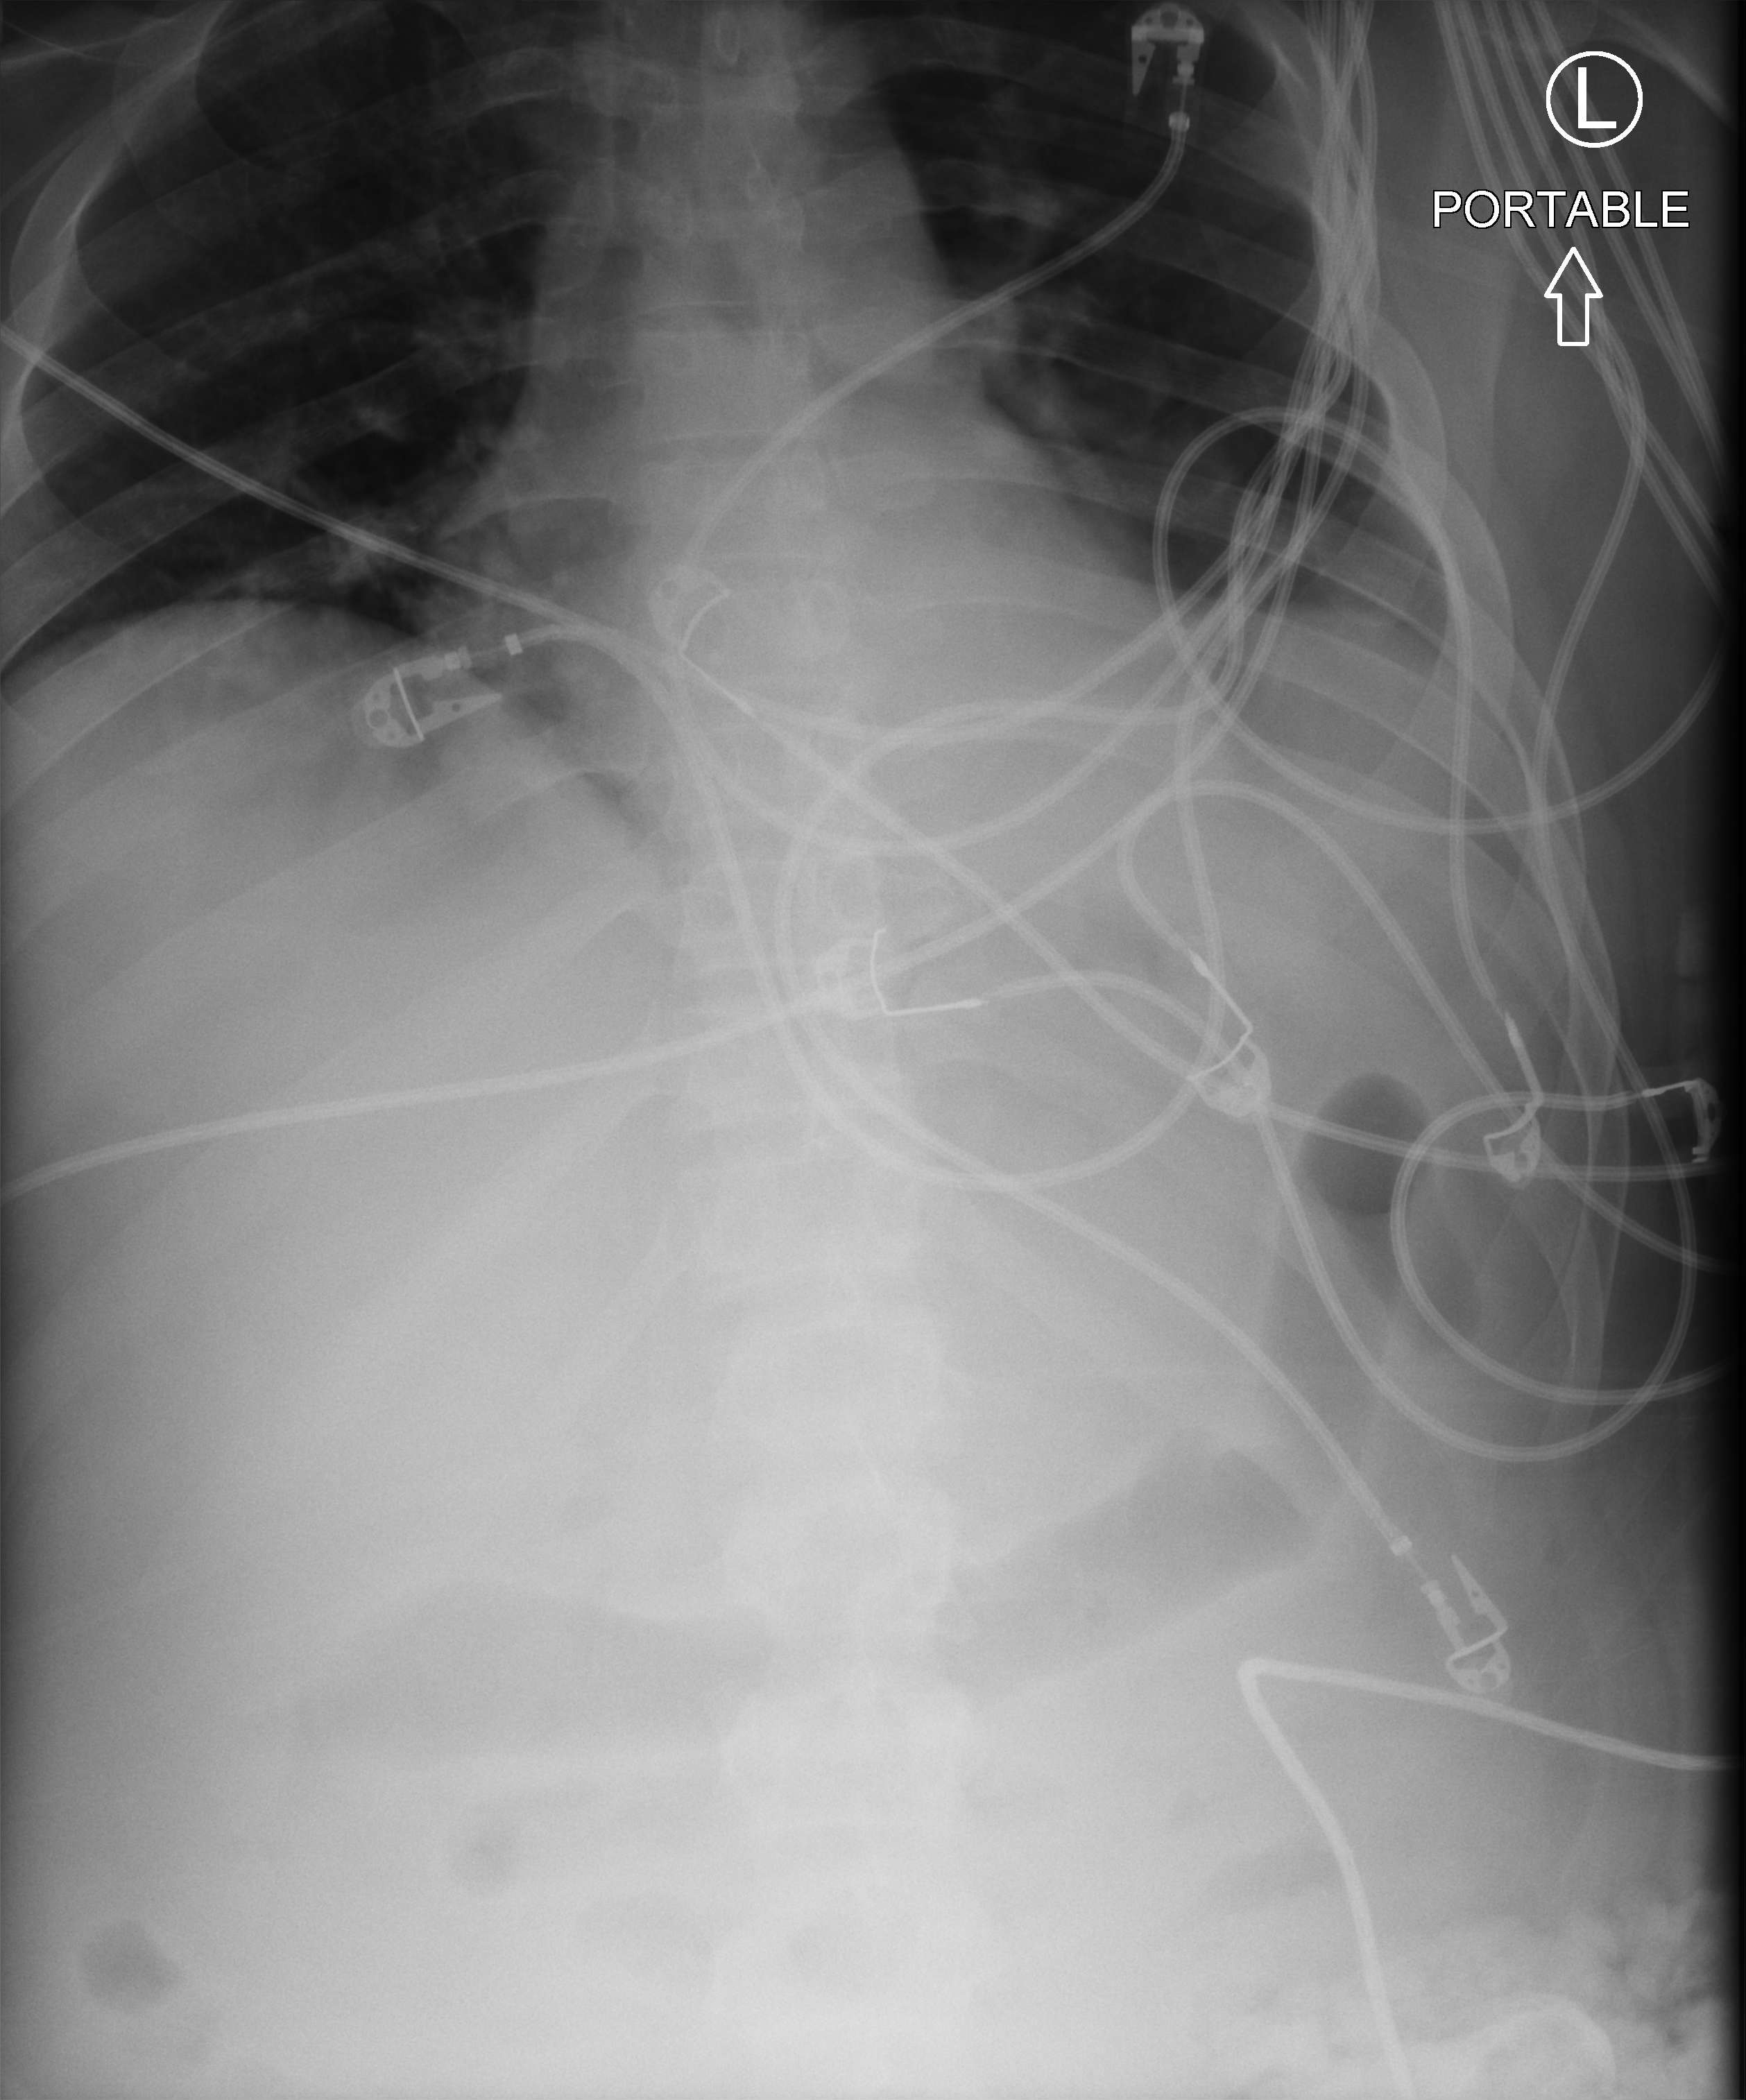
Abdomen X-ray (portable); anteroposterior (AP) projection. Patient hospitalised with COVID-19; male, aged 18–59 years.
From the hospital-stay record, not from the radiograph (when in the stay this image was taken is not recorded):
- mechanically ventilated during this hospital stay: yes
- admitted to intensive care during this hospital stay: yes
- length of hospital stay: 61 days